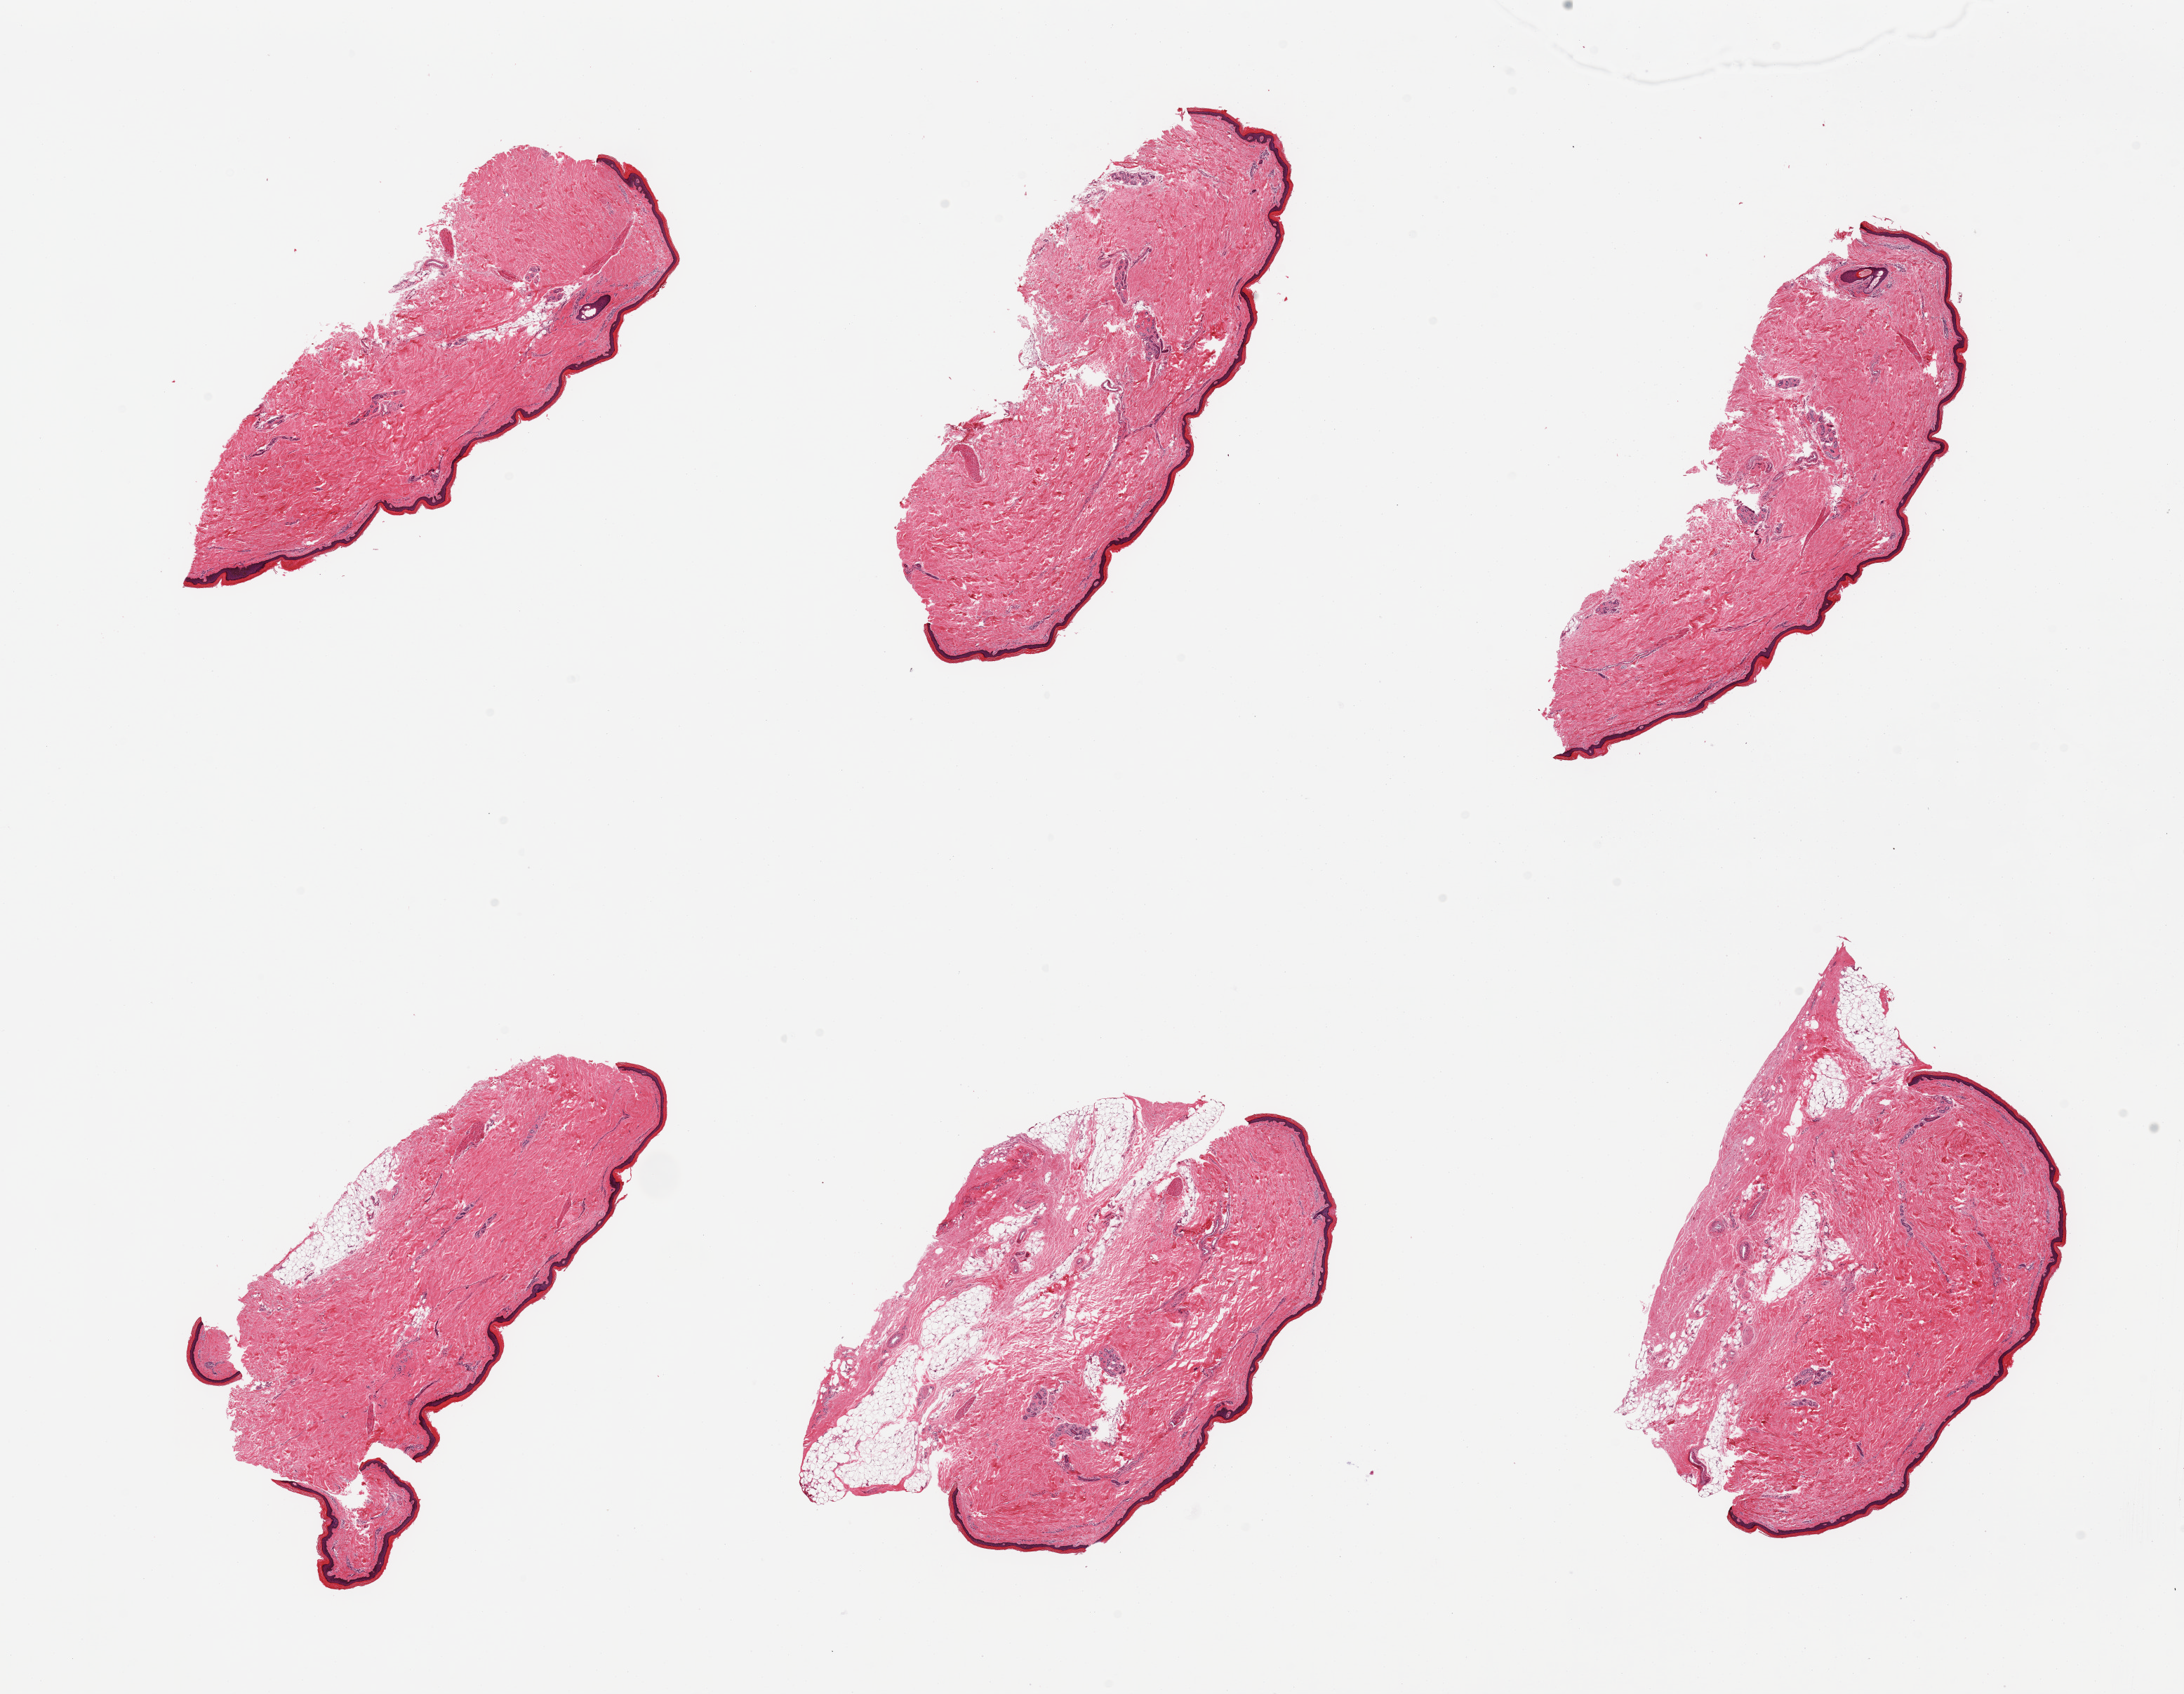
Digitized haematoxylin and eosin-stained section, brightfield — a low-resolution overview of the entire scanned area, about 24.6 x 19.1 mm. PAXgene-fixed, paraffin-embedded tissue. Section of skin of lower leg (target tissue). Tissue donor sample.
Pathologist's review note for this sample: 6 pieces, minimal dermal fat, squamous epithelium is ~40 microns.